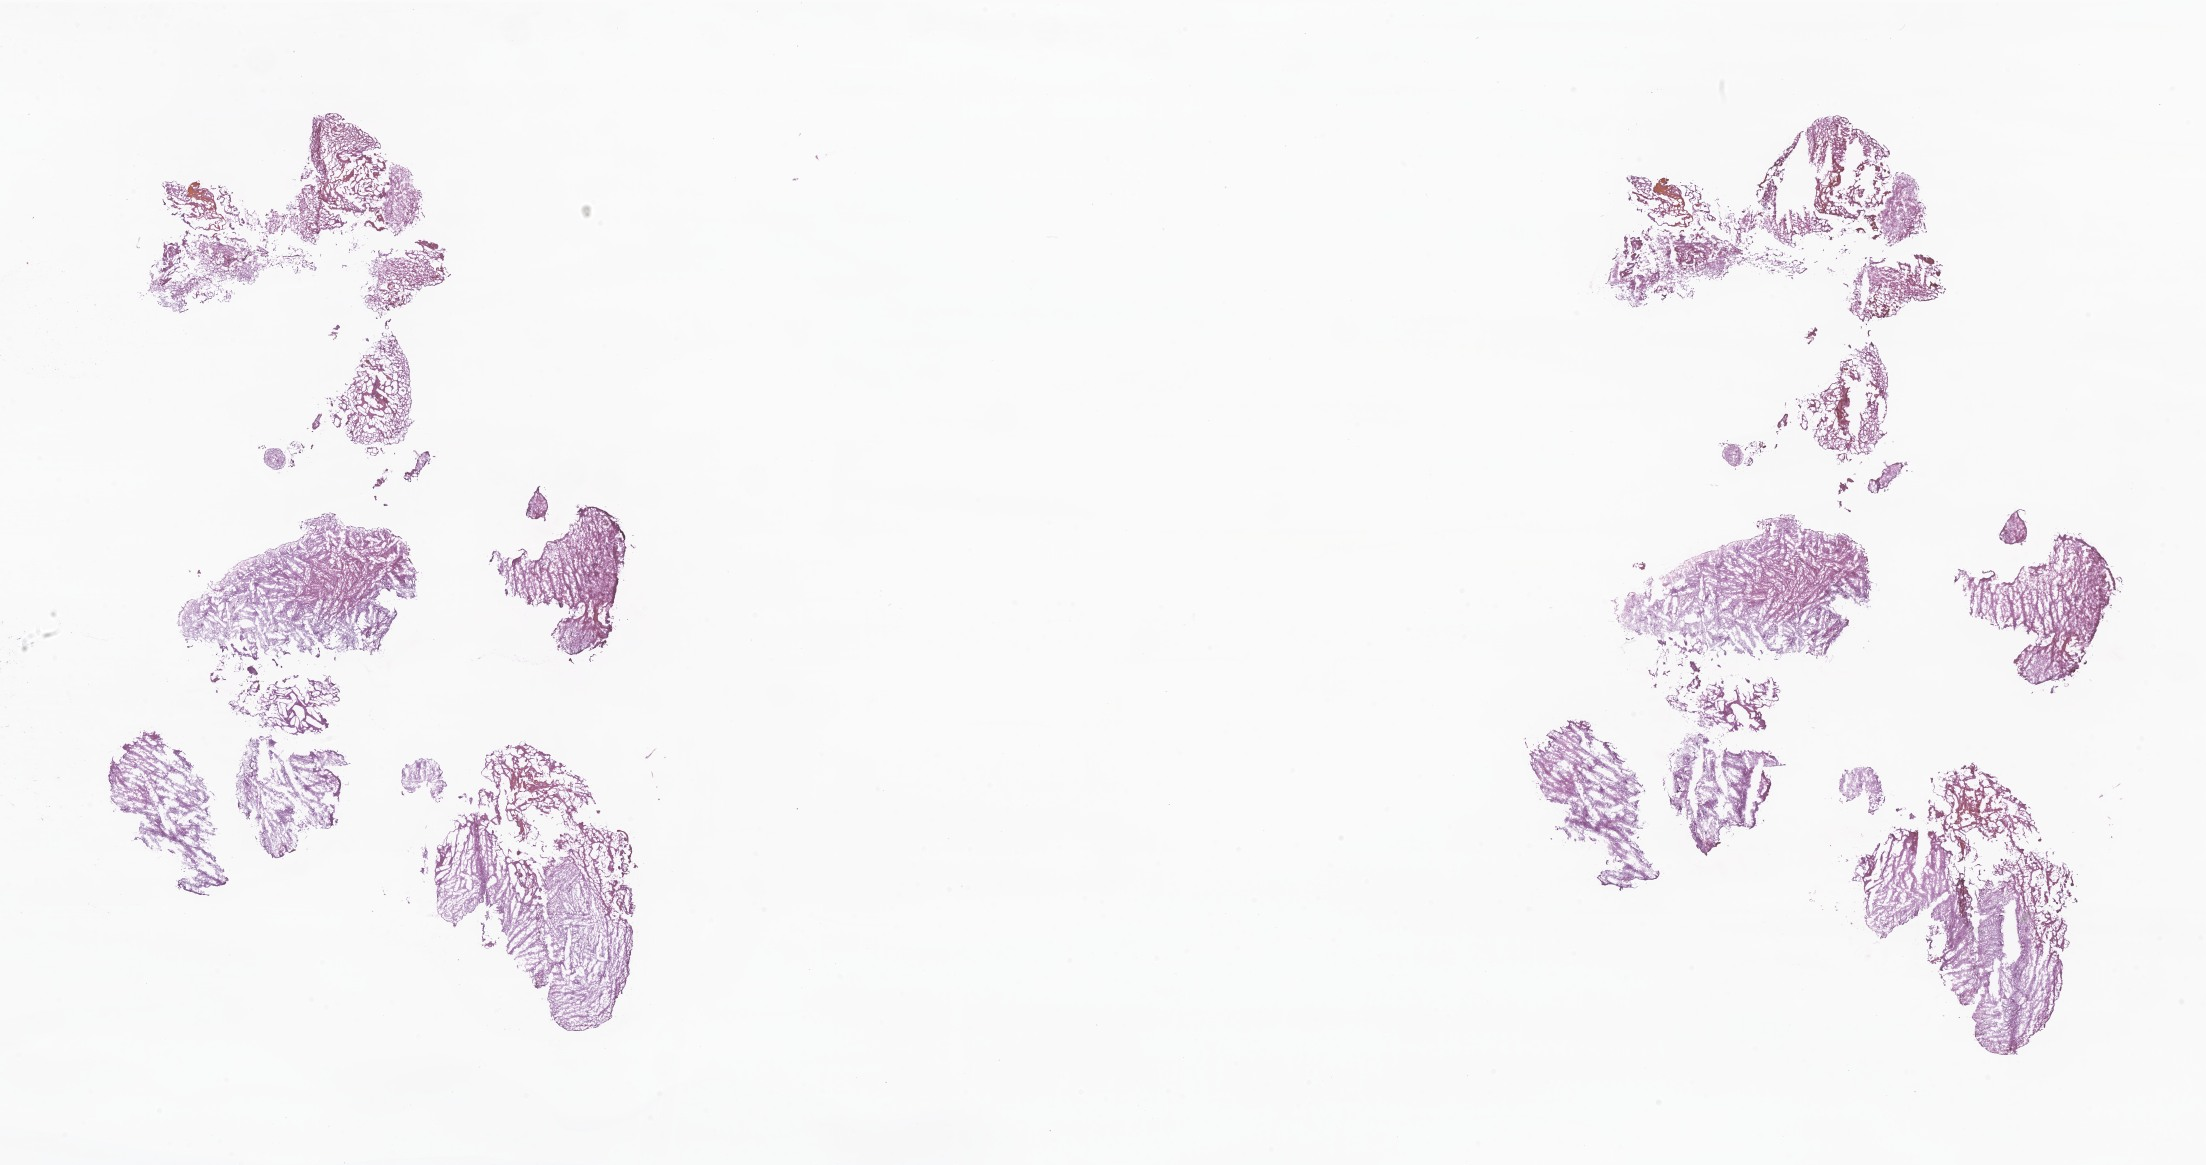
Haematoxylin and eosin whole-slide image of tumor tissue from the brain — low-resolution overview of the scanned area, about 37.2 x 19.7 mm, frozen section. Patient male; age 87 months (7 years 3 months).
• diagnosis: Neoplasm, uncertain whether benign or malignant